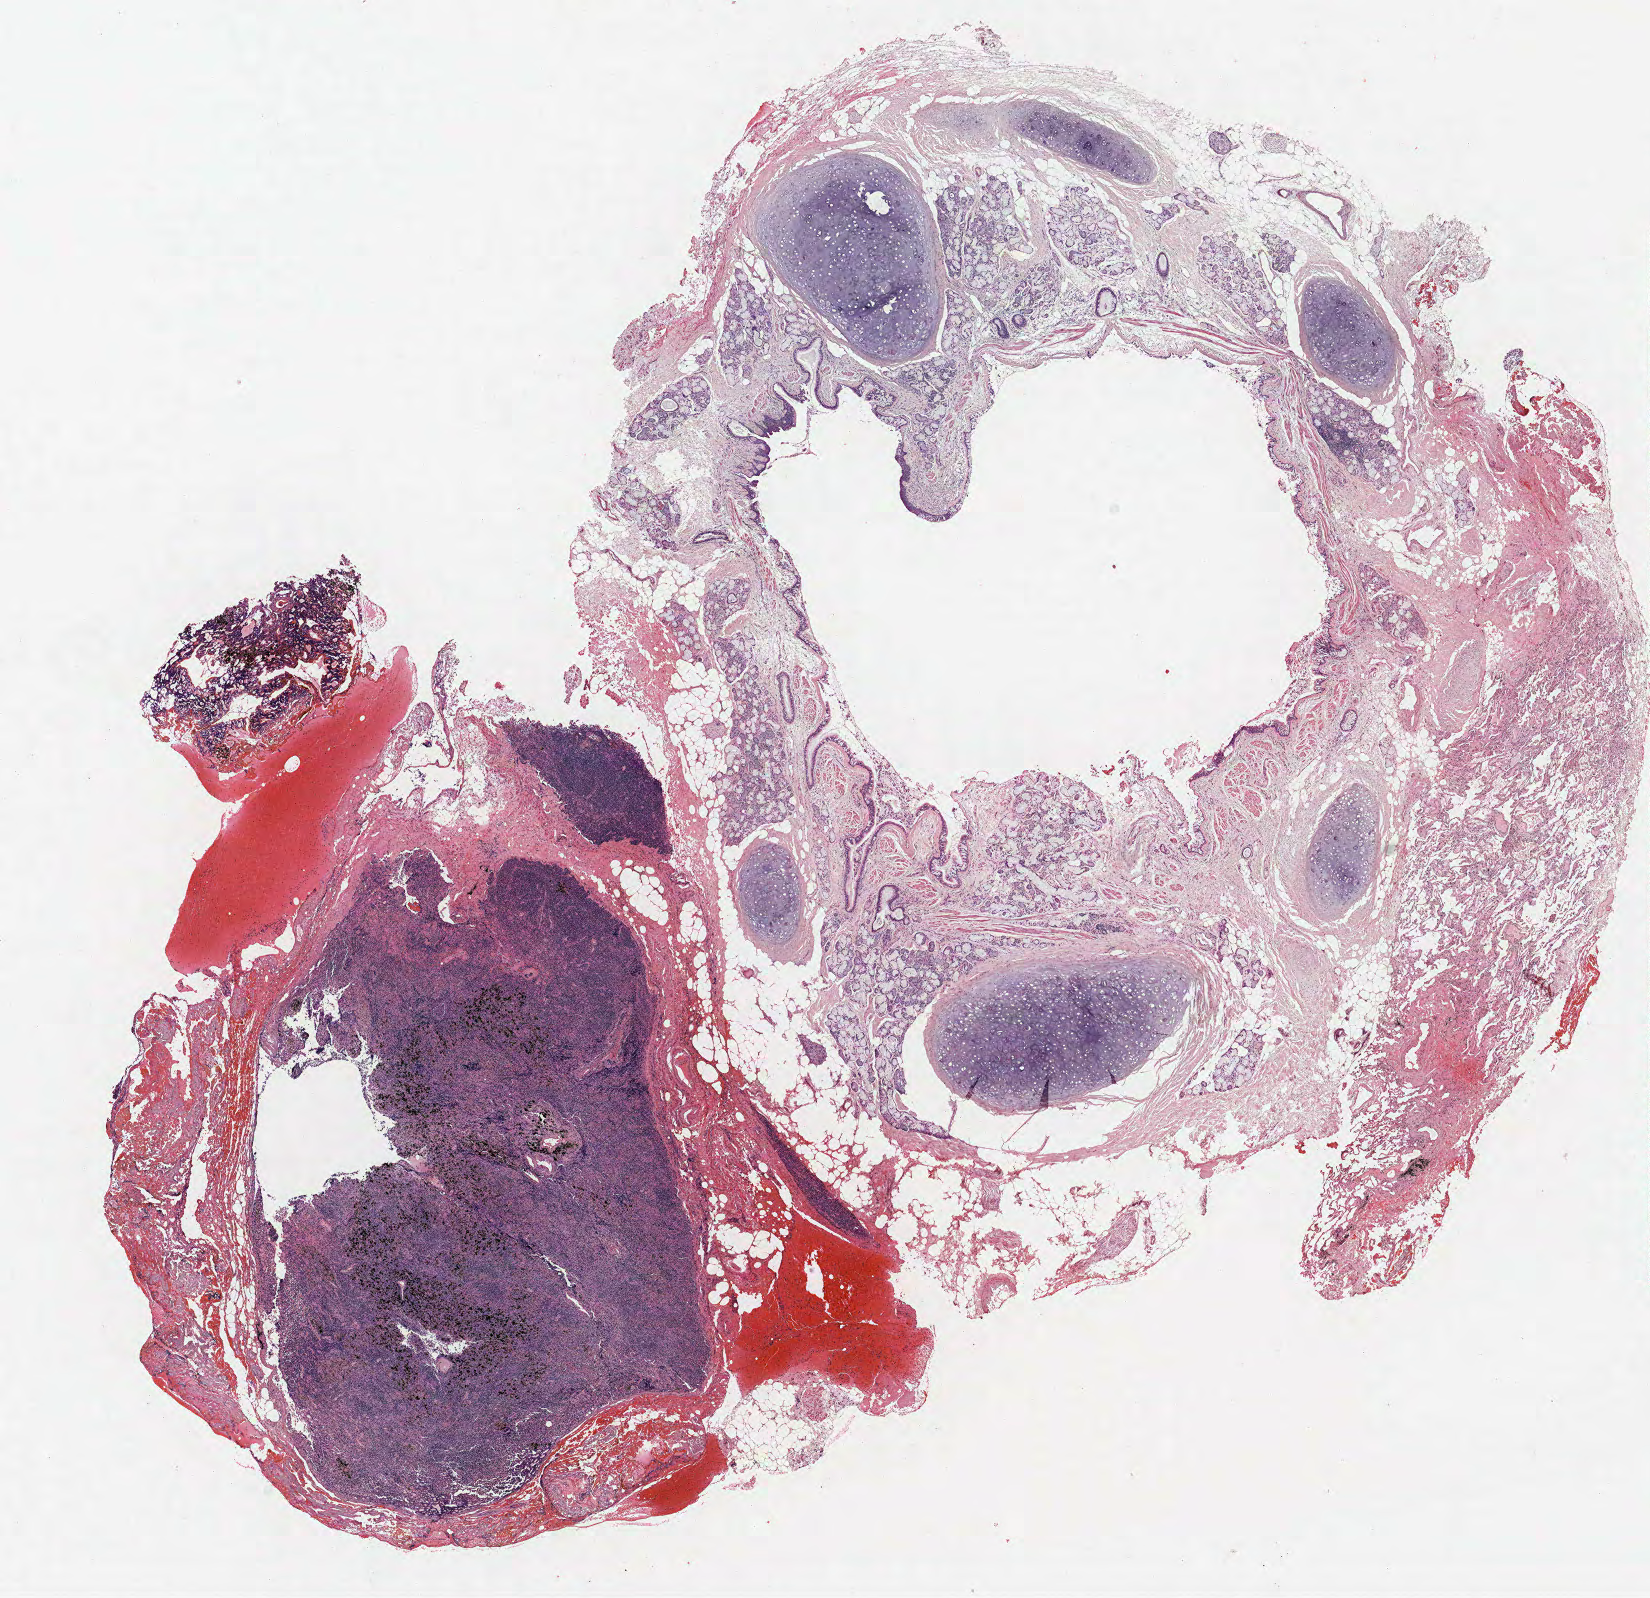
Whole-slide histology image, H&E — shown as a low-resolution overview of the whole scanned area (about 13.2 x 12.8 mm), formalin-fixed paraffin-embedded (FFPE) section, lung tissue. Female patient, aged 66 at enrolment. Current smoker at enrolment.
Participant's lung-cancer diagnosis: Bronchiolo-alveolar carcinoma, mucinous (ICD-O-3 8253/3).